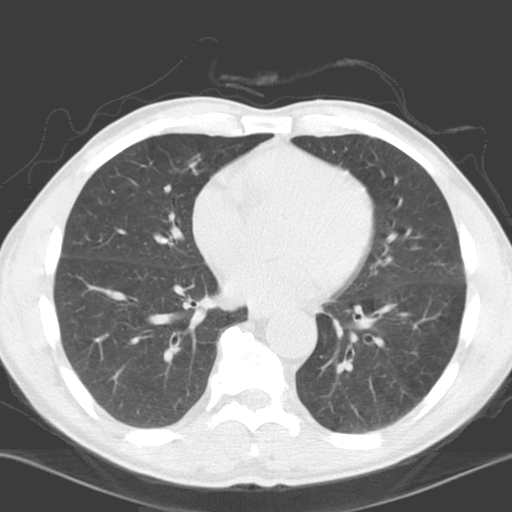
Axial slice from a low-dose chest CT screening exam. Baseline annual screen. Lung window (W 1500 / L -600 HU). 3.2 mm slice thickness. Standard (soft-tissue) reconstruction kernel (C). Male, age 65 years at enrolment. Current smoker at enrolment.
- Lesion marked by an expert reader, bounding box (x1, y1, x2, y2) in pixels: (150, 148, 209, 213).
- Screening reader's record for this exam (one nodule recorded; not confirmed to be the boxed lesion): non-calcified nodule or mass ≥4 mm, right lower lobe, 5 × 5 mm, poorly defined margins, soft tissue attenuation.
- Participant outcome: lung cancer diagnosed 1144 days after this screen — squamous cell carcinoma, NOS, right middle lobe, poorly differentiated (G3), stage IA (AJCC 6th edition), 23 mm at pathology.